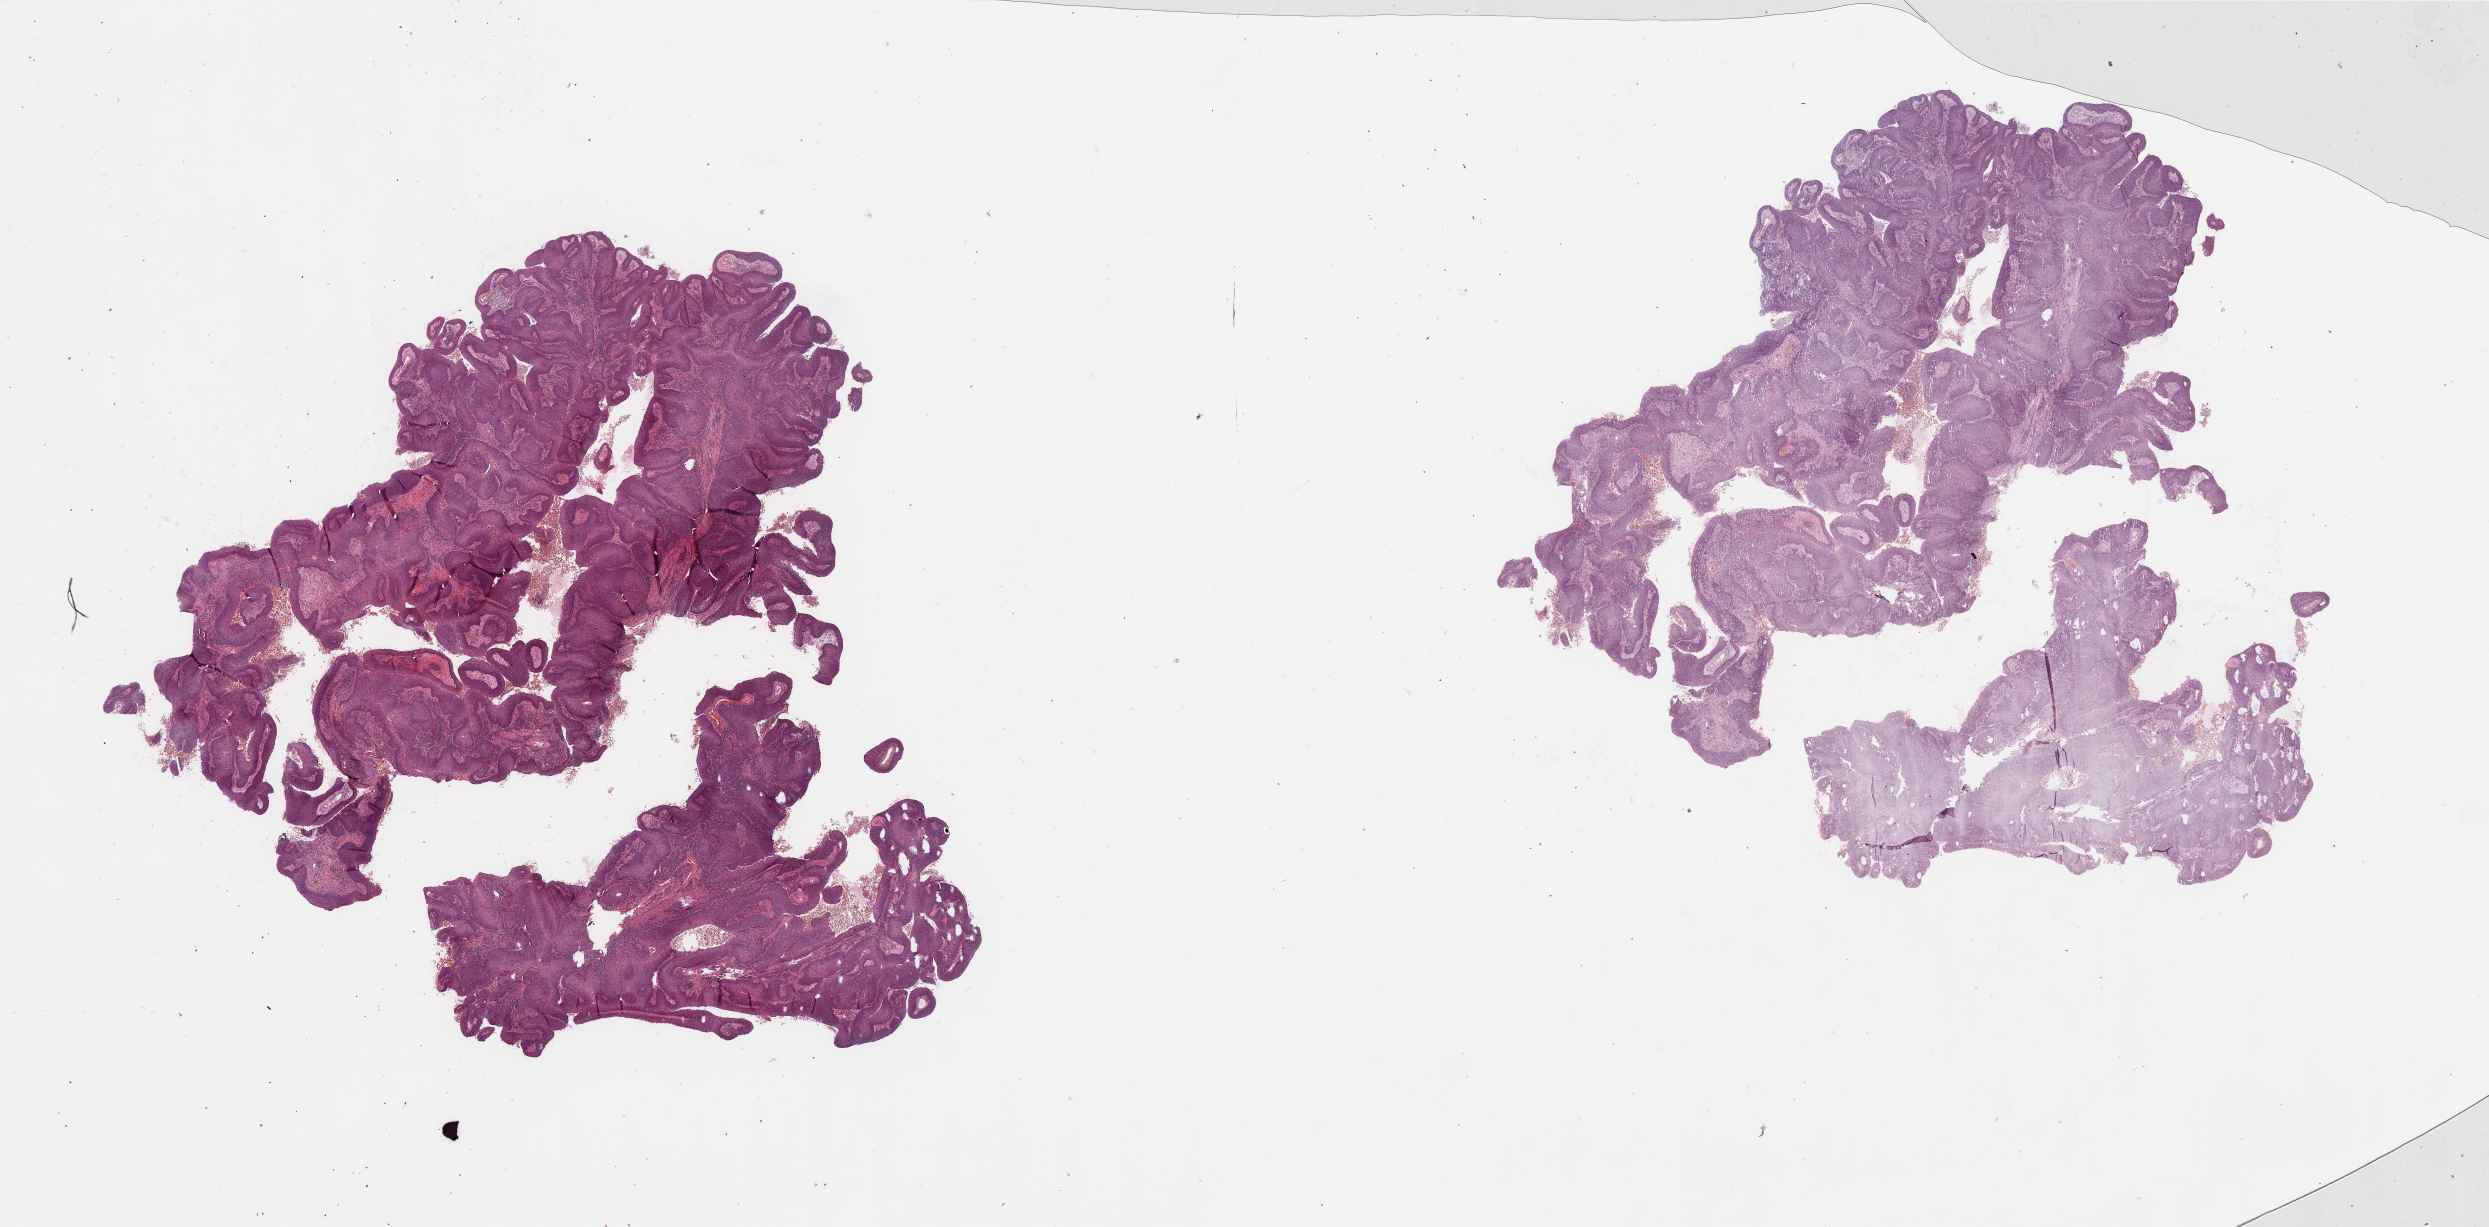
H&E whole-slide image, a low-resolution overview of the entire scanned area, about 39.4 x 19.4 mm. Lung, tumour tissue. 68-year-old male patient.
Patient diagnosis (cohort enrolment): squamous cell carcinoma (lung).